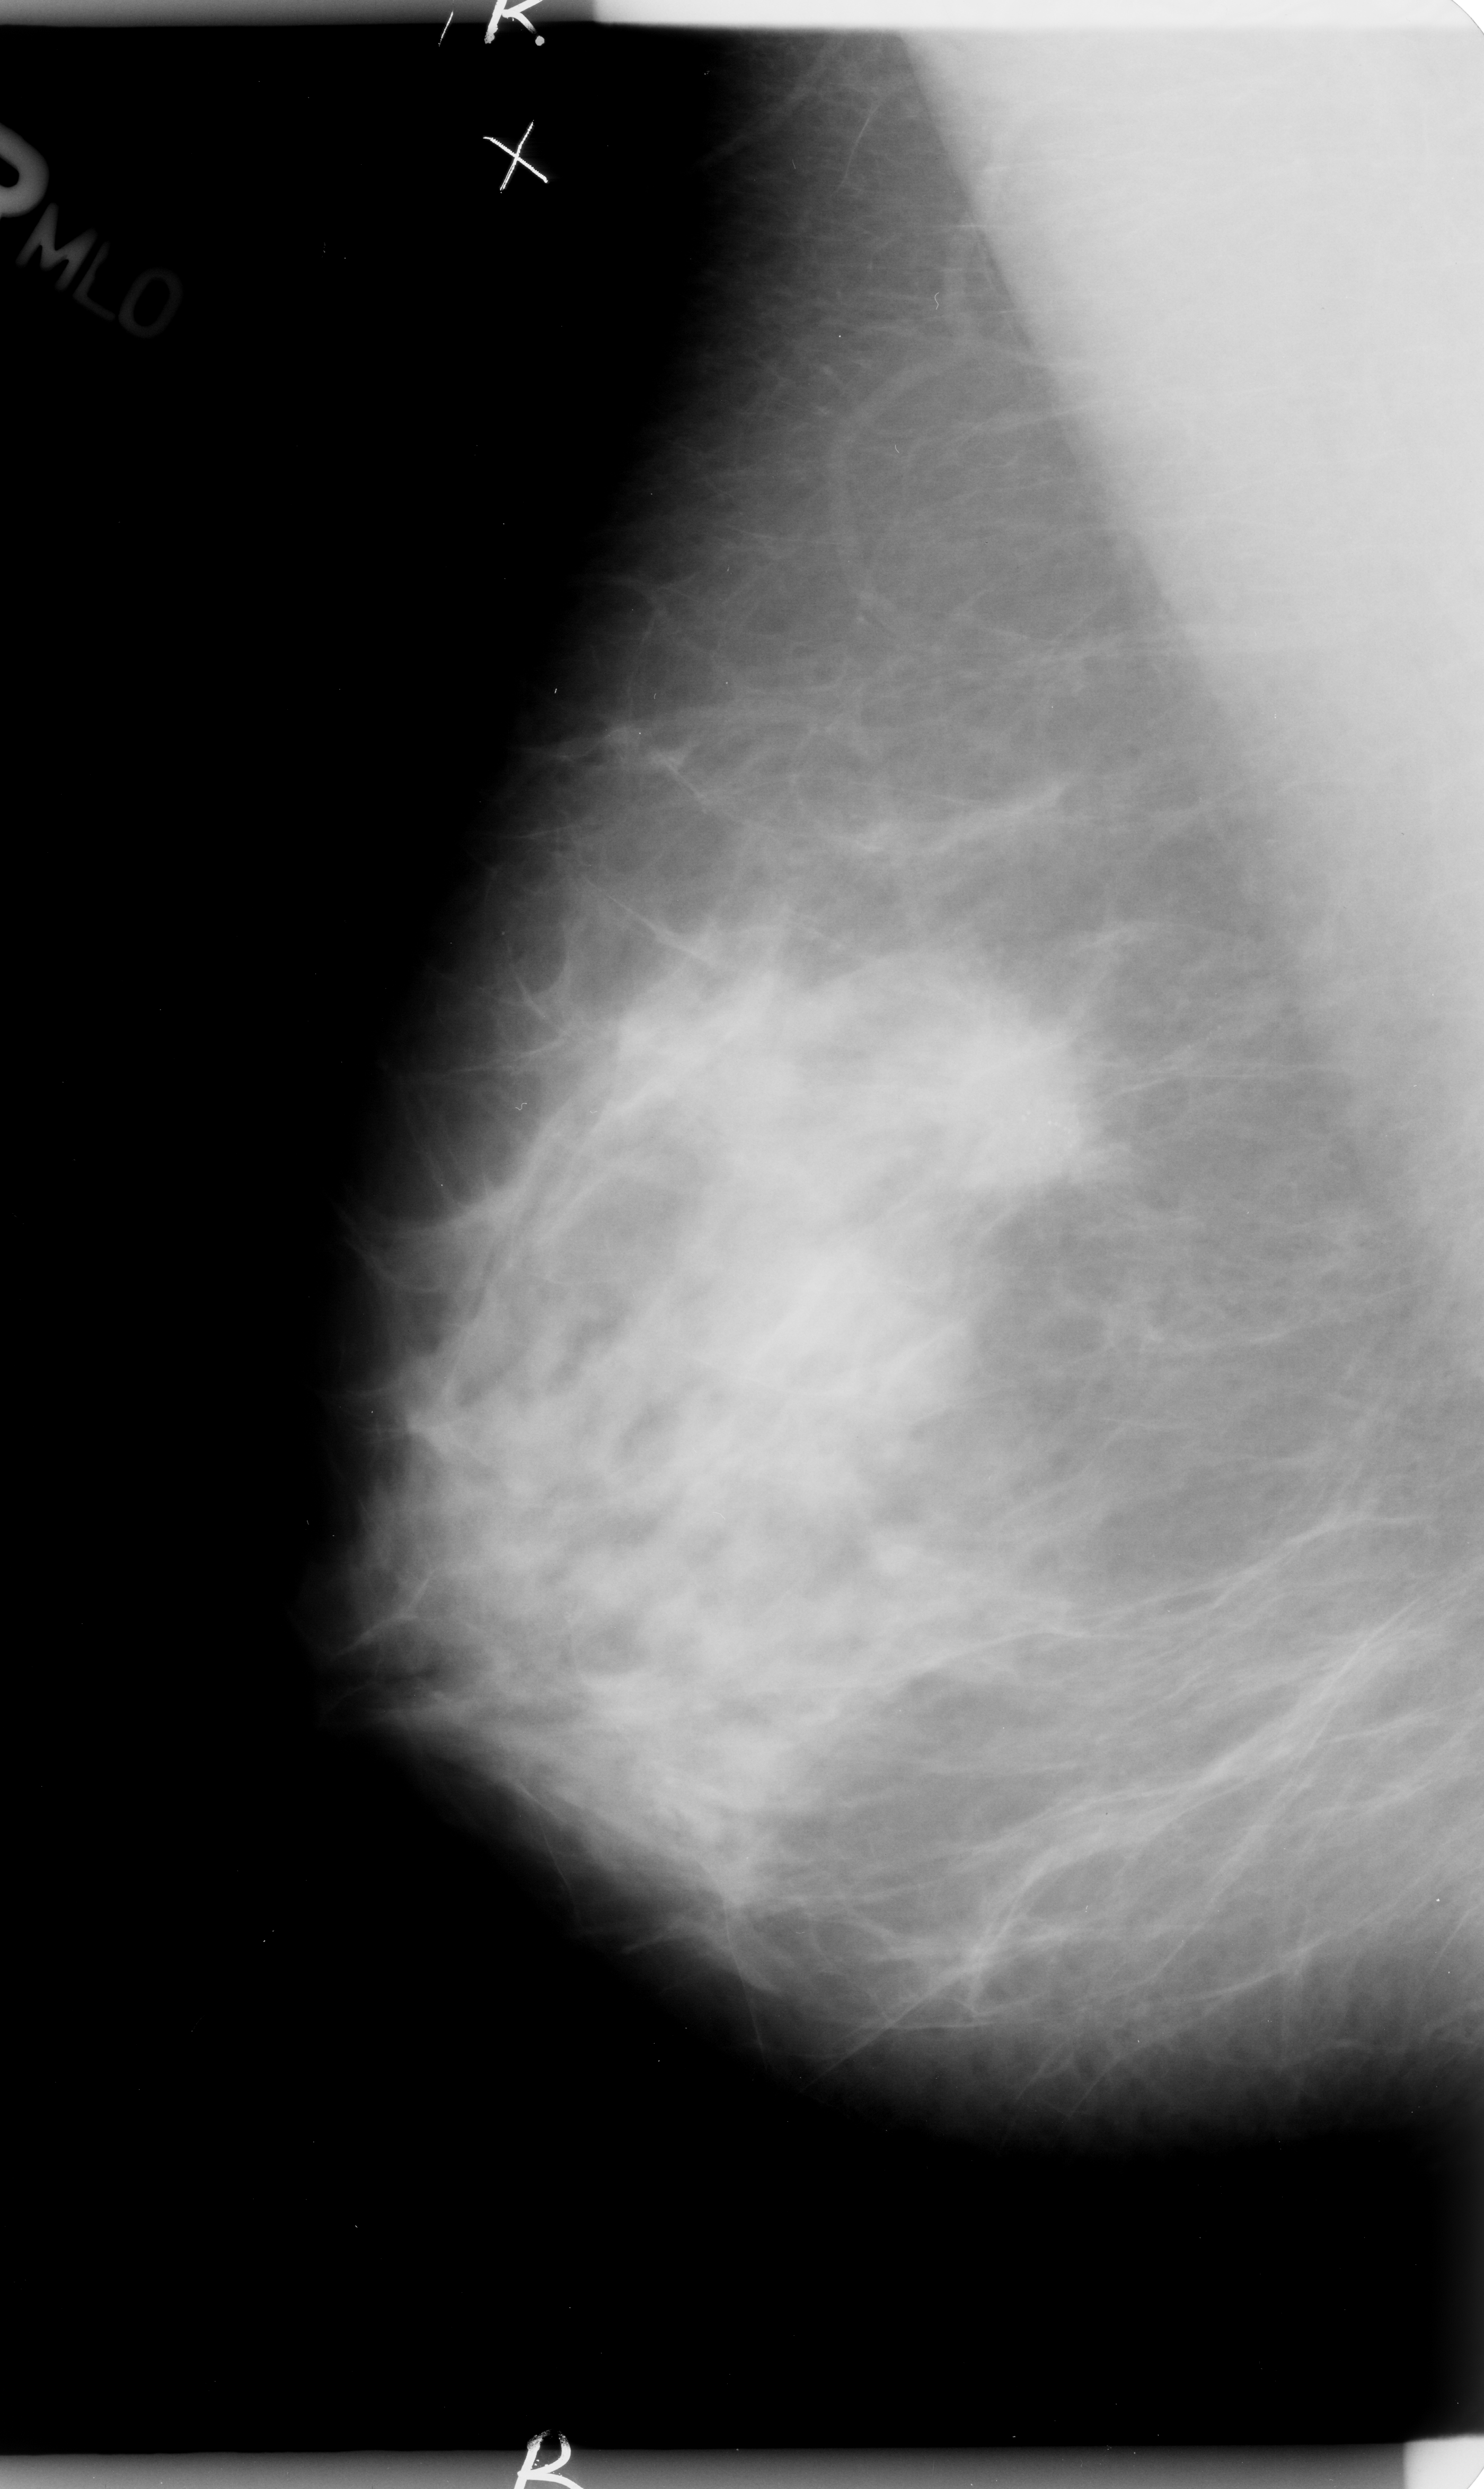
Mammogram (digitized film); right breast; mediolateral oblique (MLO) view; BI-RADS breast density category 3 (scale 1–4); 1484 × 2489 image matrix.
Expert-marked regions of interest on this film, with their recorded descriptors:
- calcifications, morphology pleomorphic, distribution clustered / linear; BI-RADS assessment category 5; pathology result (as recorded, not read from the image): malignant: box from (x=843, y=937) to (x=1146, y=1218) px